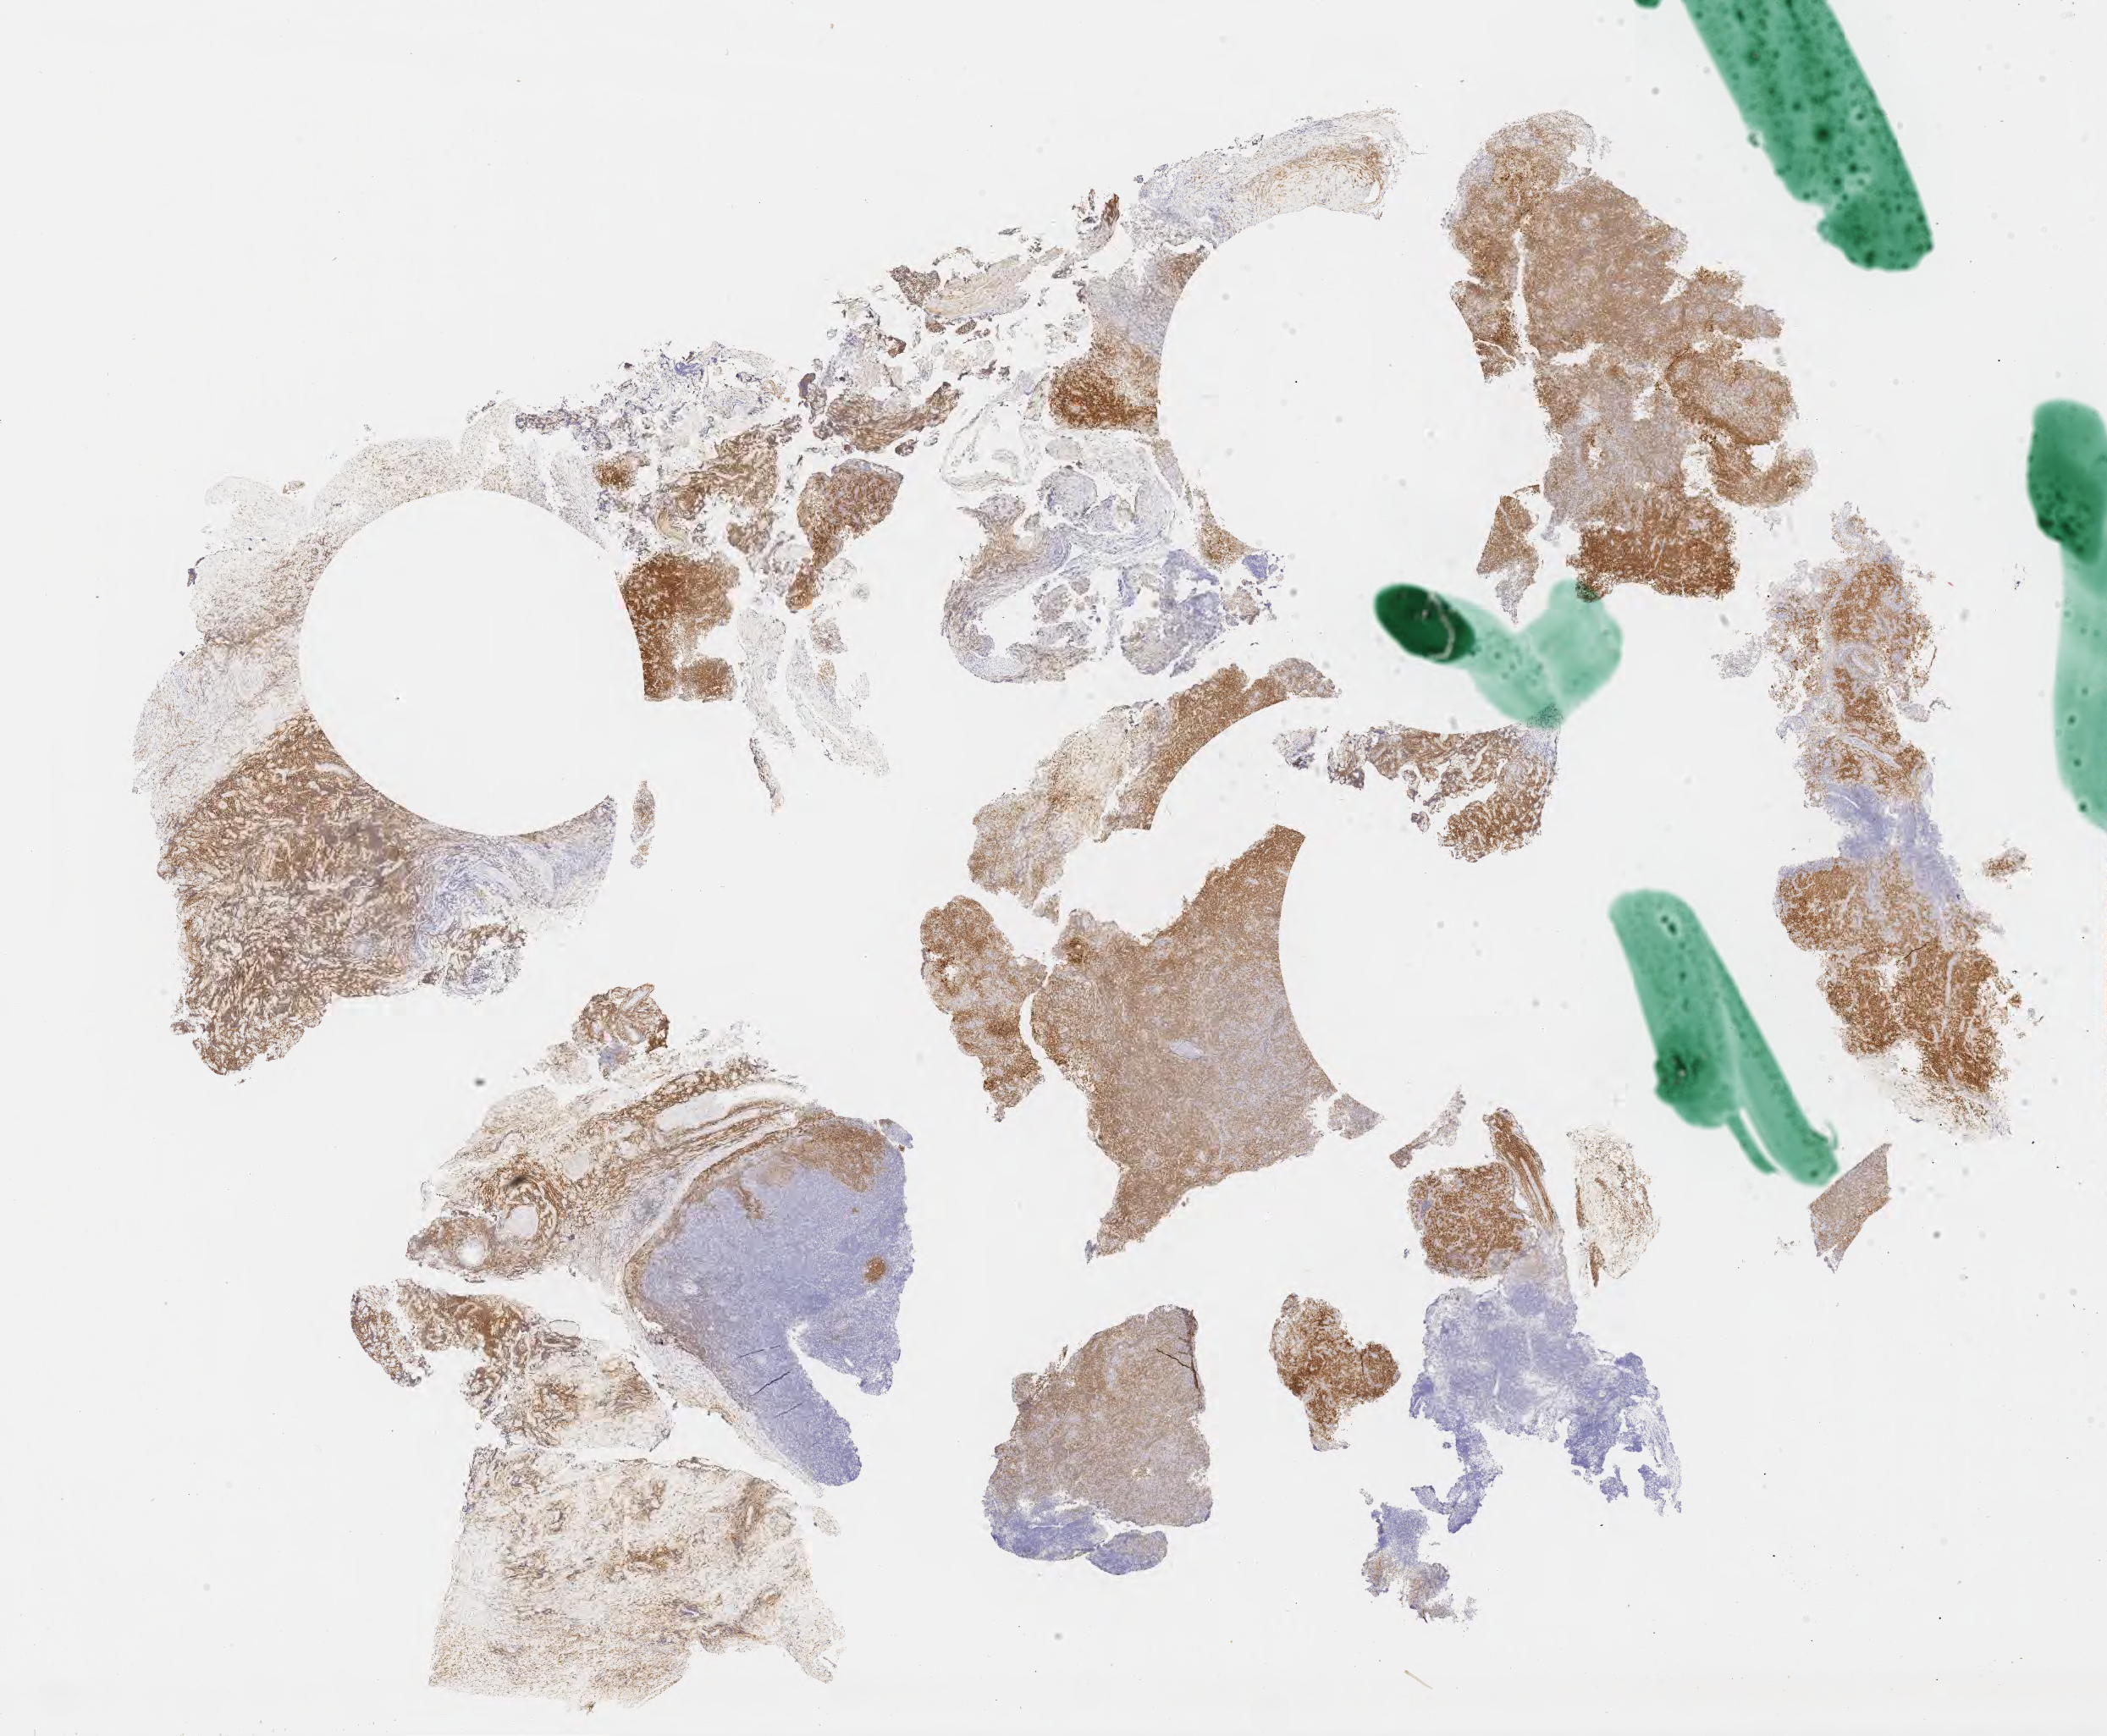
Whole-slide image, immunohistochemical stain for CD10 — low-resolution overview of the scanned area, about 20.1 x 16.6 mm, specimen: tumor tissue, anatomic site: lymph node. Patient: male, aged 29.
Histologic diagnosis: Diffuse large B-cell lymphoma, NOS.